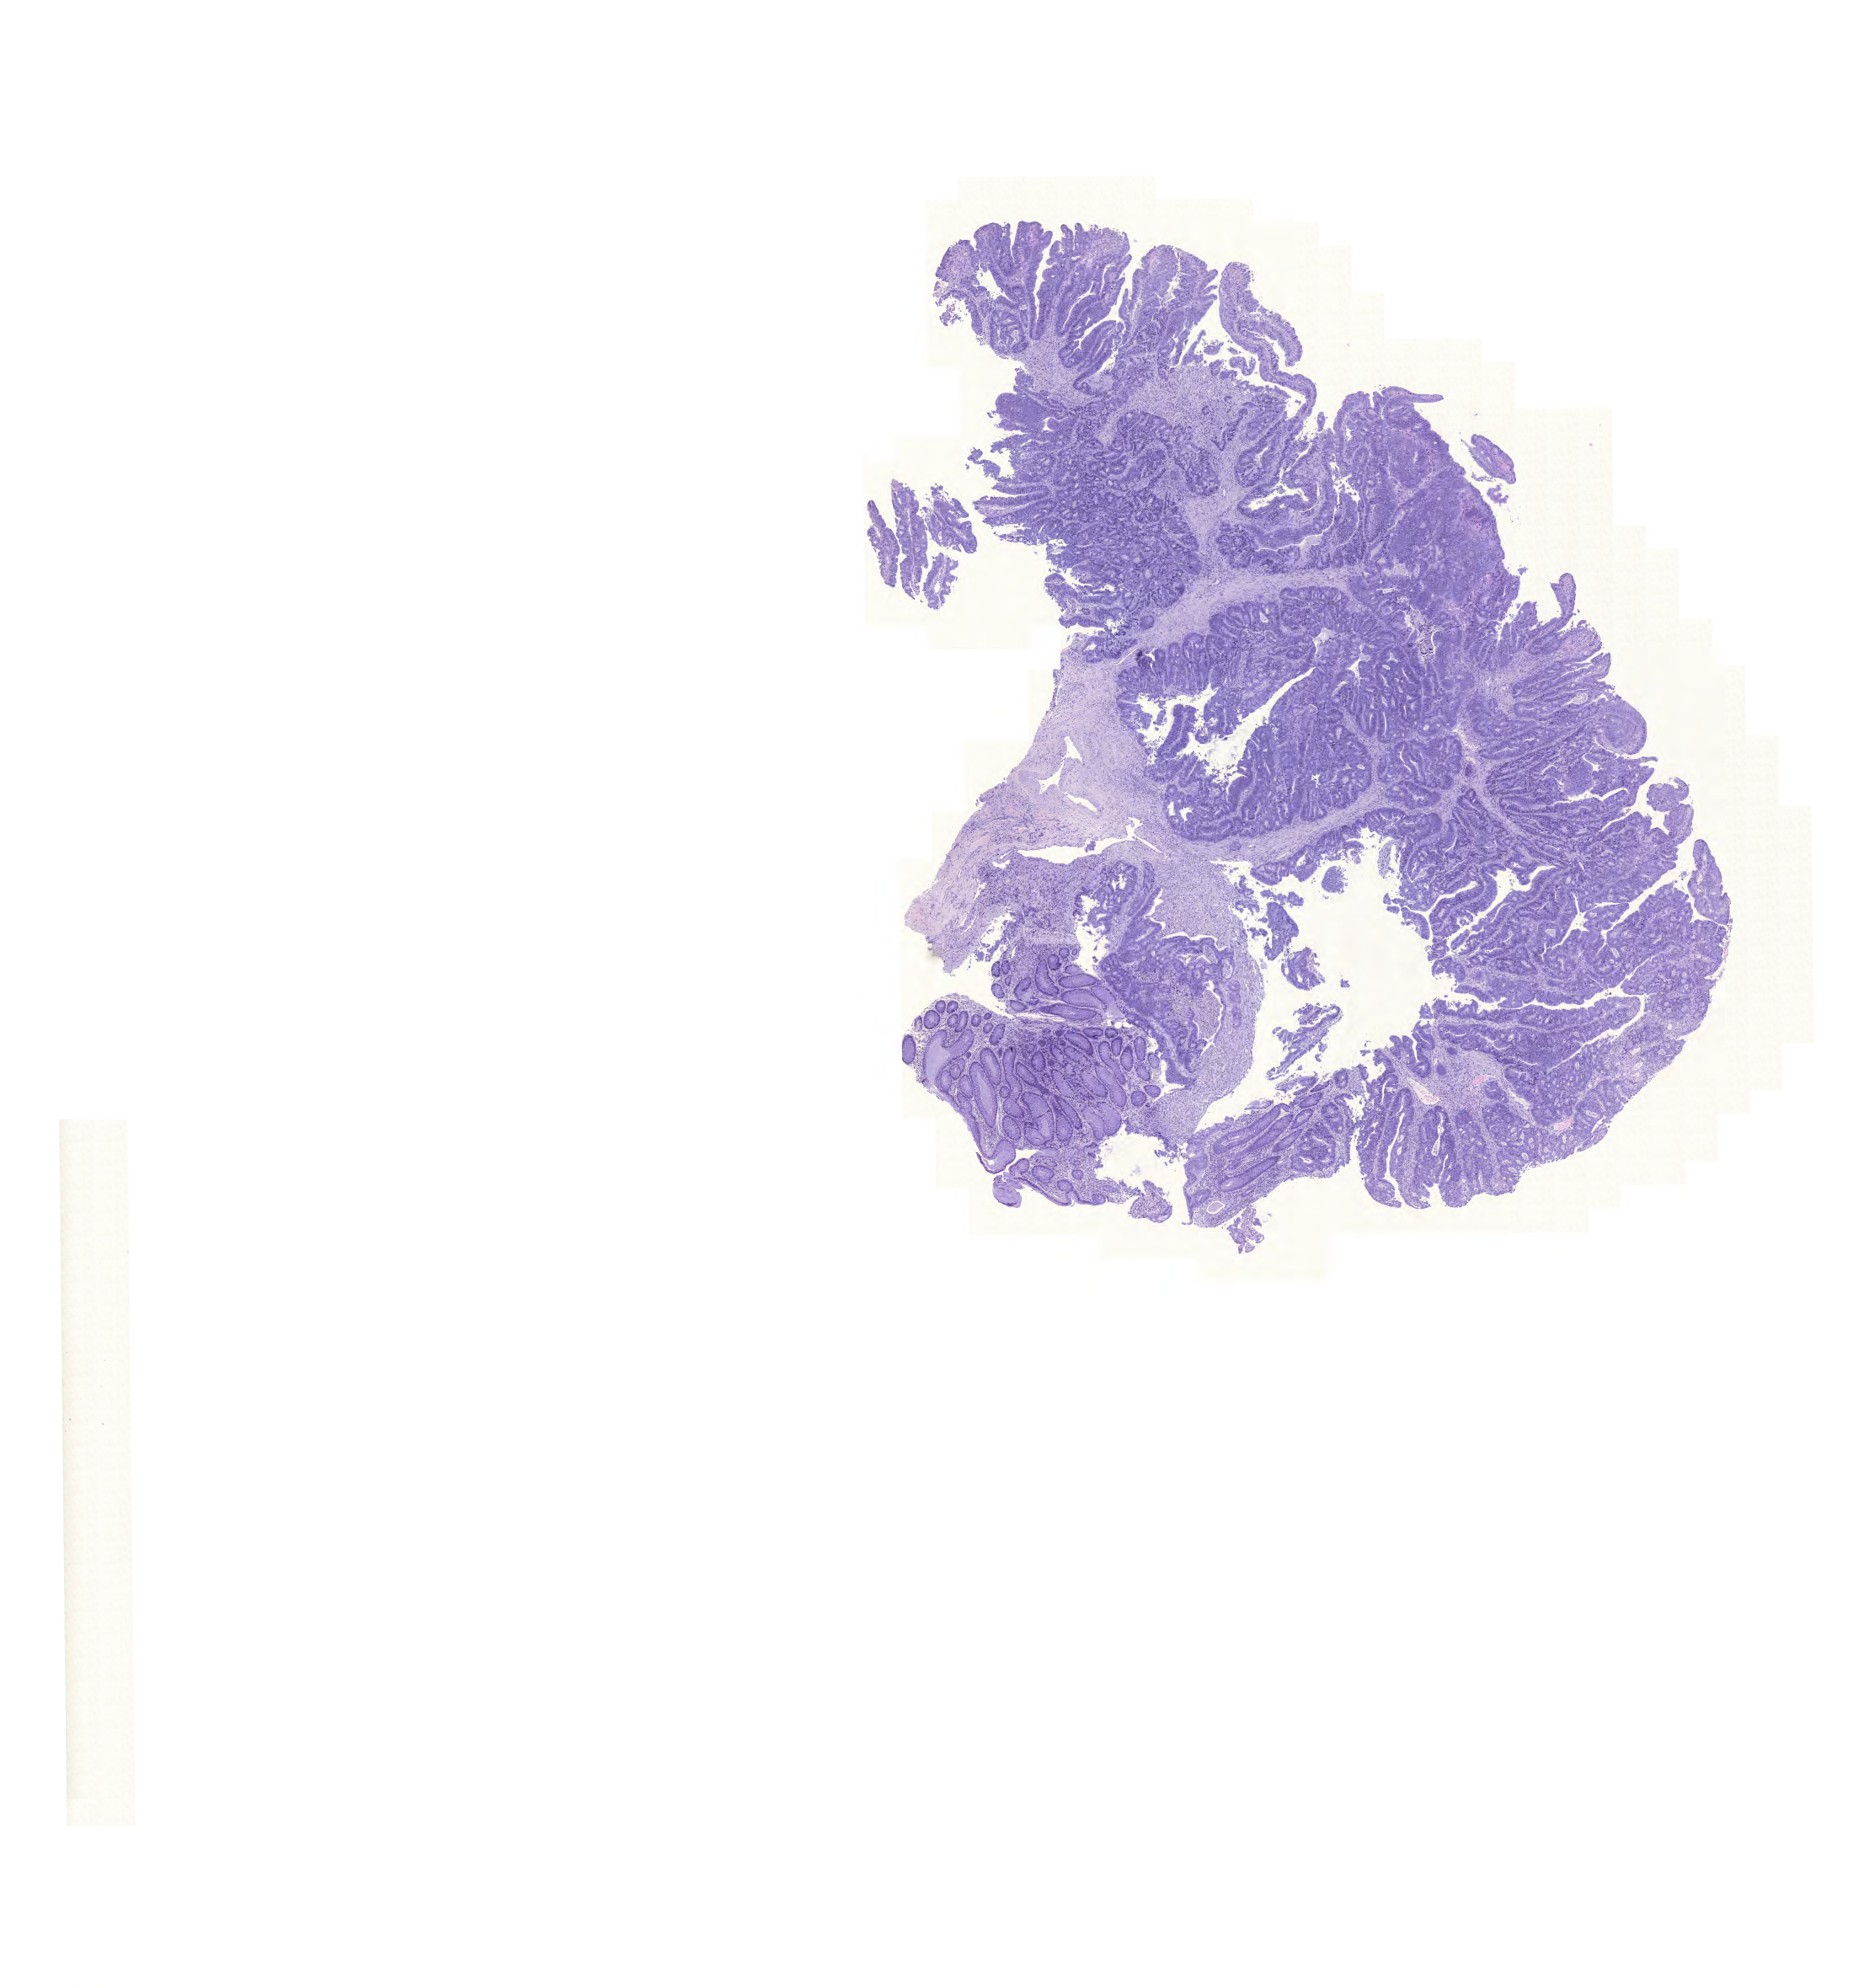
Hematoxylin and eosin (H&E) stained whole-slide image, shown as a low-resolution overview of the whole scanned area (about 16.4 x 17.6 mm, acquisition: 20x scan); formalin-fixed paraffin-embedded (FFPE) diagnostic section; primary tumour sample from the colon. Male patient; age at initial diagnosis 84 years.
• pathologic diagnosis: Adenocarcinoma, NOS (sigmoid colon)
• AJCC pathologic stage: IIA